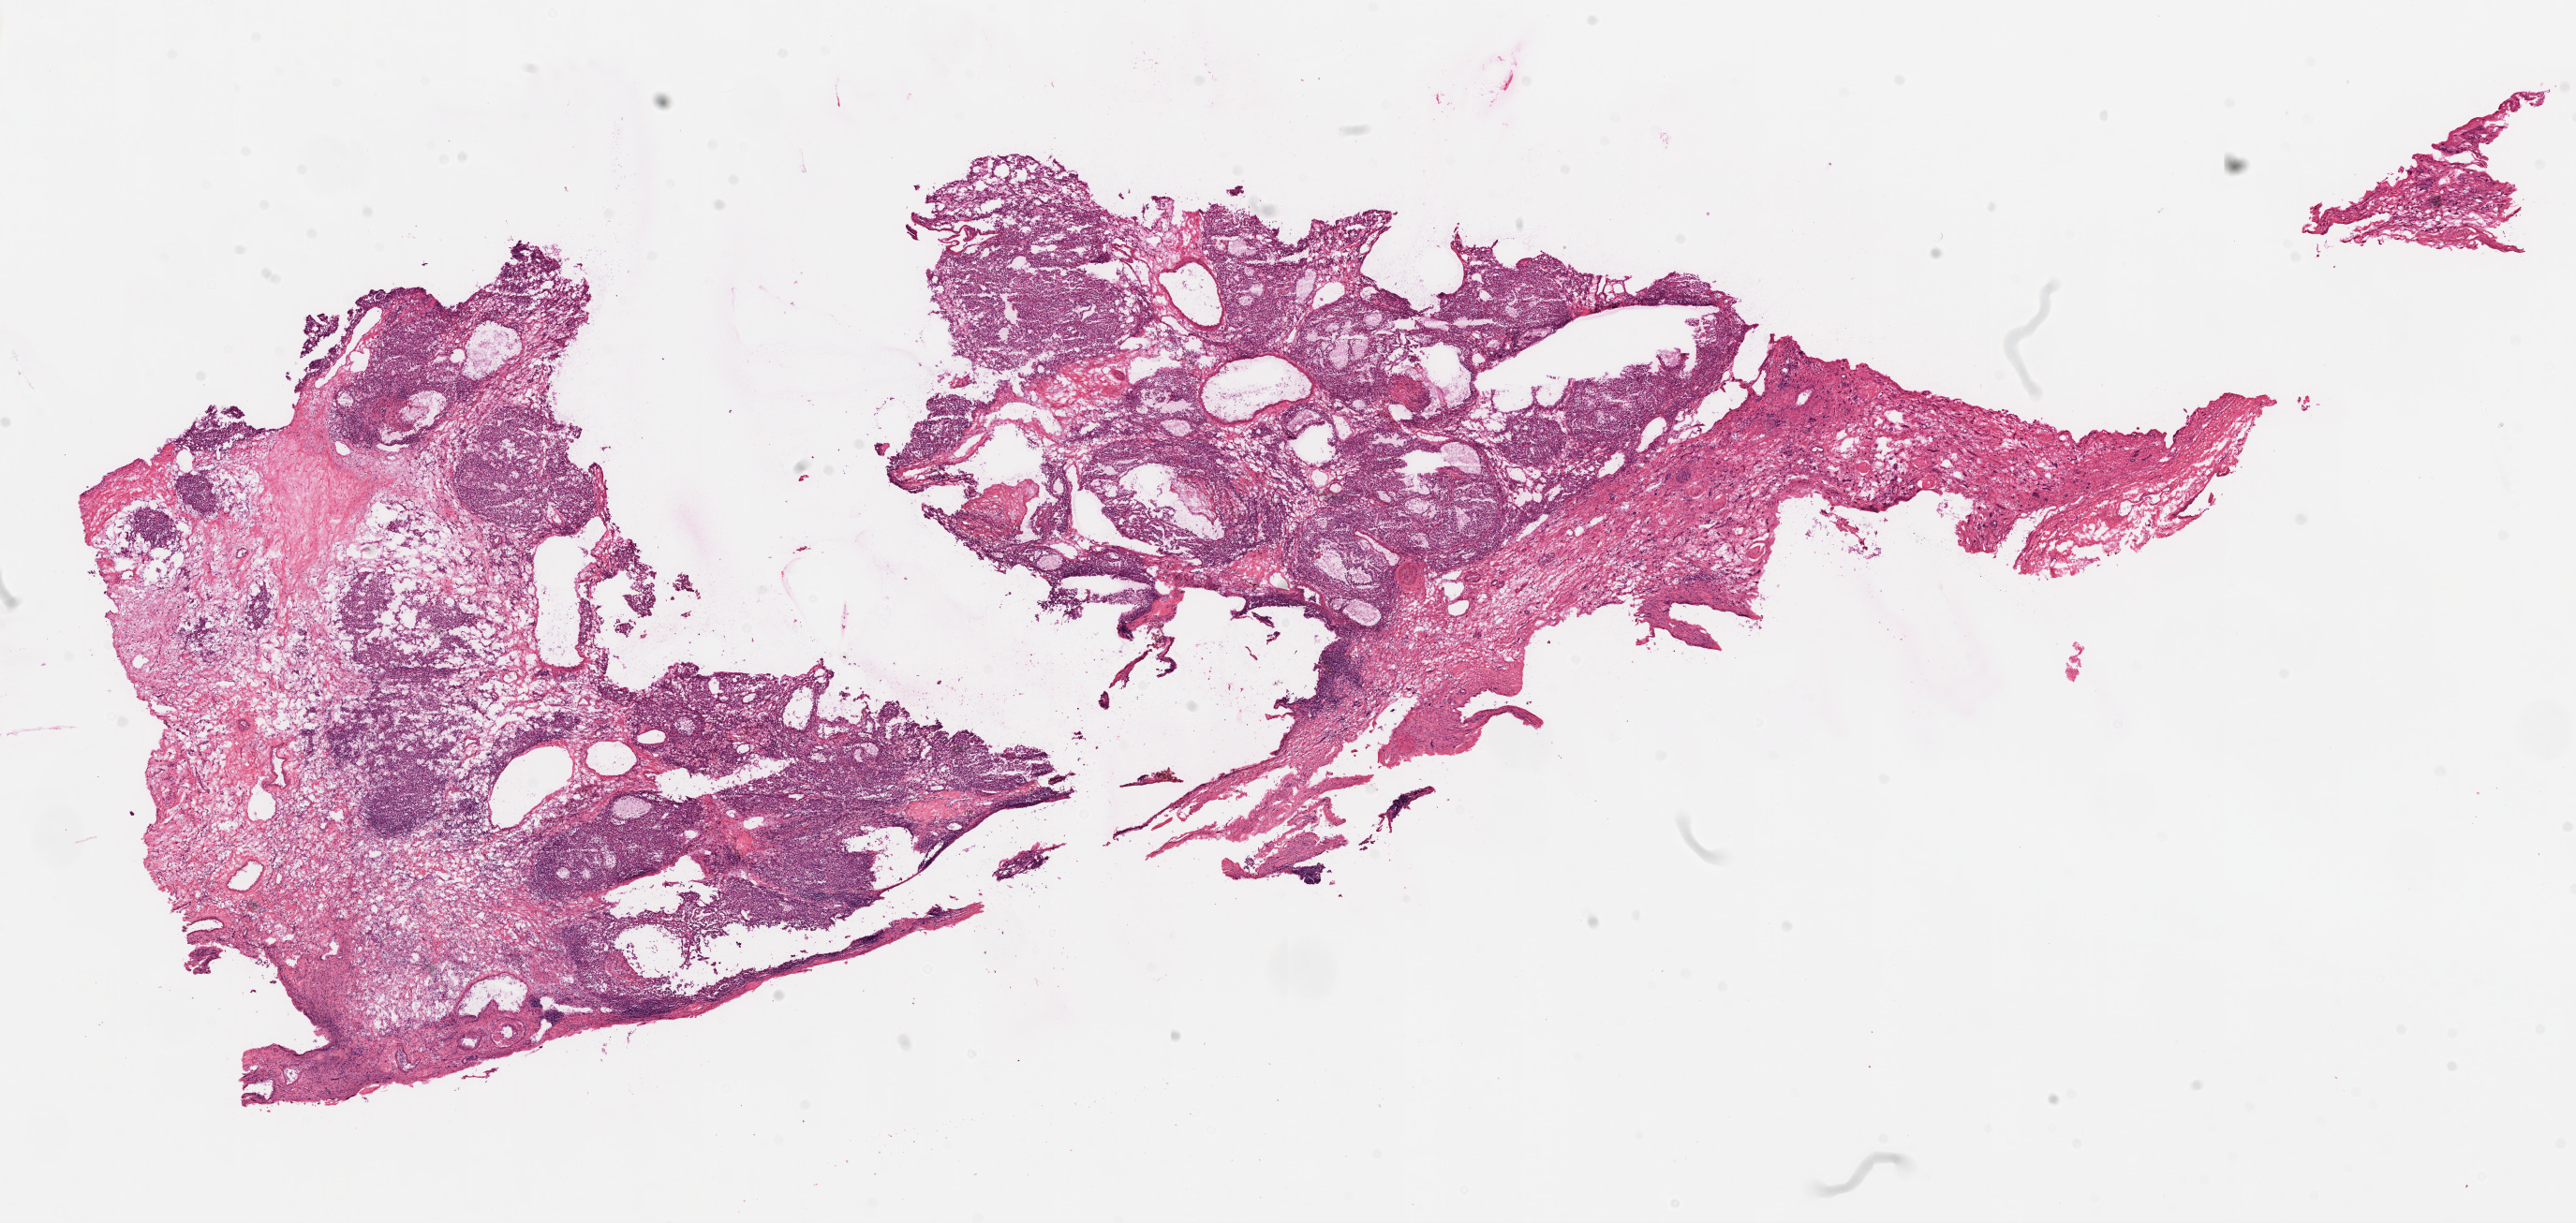
Whole-slide histology image, H&E — shown as a low-resolution overview of the whole scanned area (about 22.1 x 10.5 mm, acquisition: 20x scan), frozen section from the top of the tissue portion, sample: primary tumour, kidney. Patient: female, age at initial diagnosis 52 years. Histologic grade: G2 (moderately differentiated). Slide review estimates, as recorded: tumour cells 70%, tumour nuclei 80%, normal cells 0%, stromal cells 30%, necrosis 0%.
- pathologic diagnosis: Clear cell adenocarcinoma, NOS
- AJCC pathologic stage: I